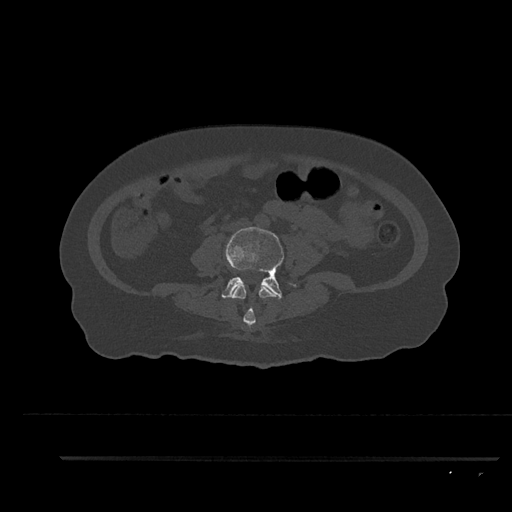
CT including the spine, one axial slice. Position 45 of 797 along the scan axis. Bone window (W 1800 / L 400 HU). 512 × 512 image matrix, field of view 408 × 408 mm. Female patient, age 44 years. Case-level facts recorded for this patient, not image findings: primary cancer: renal.
Annotated regions visible in this slice (semi-automatically segmented with operator editing):
- L3 vertebra: bounding box [x1, y1, x2, y2] px = [232, 285, 281, 329]
- L4 vertebra: [222, 227, 296, 299]